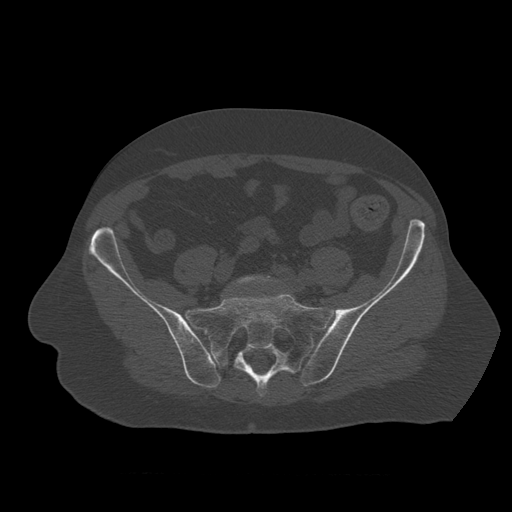
CT including the spine, one axial slice. Slice 233 of 450 in the series (ordered by position). 120 kVp. Bone window (W 1800 / L 400 HU). 512 × 512 image matrix, field of view 405 × 405 mm. Patient age 75 years. From the clinical record (not read from this slice): primary cancer: prostate.
Annotated regions visible in this slice (semi-automatic segmentation, software-assisted and operator-edited):
- L5 vertebra: bounding box (x1, y1, x2, y2) in pixels: (222, 276, 276, 297)